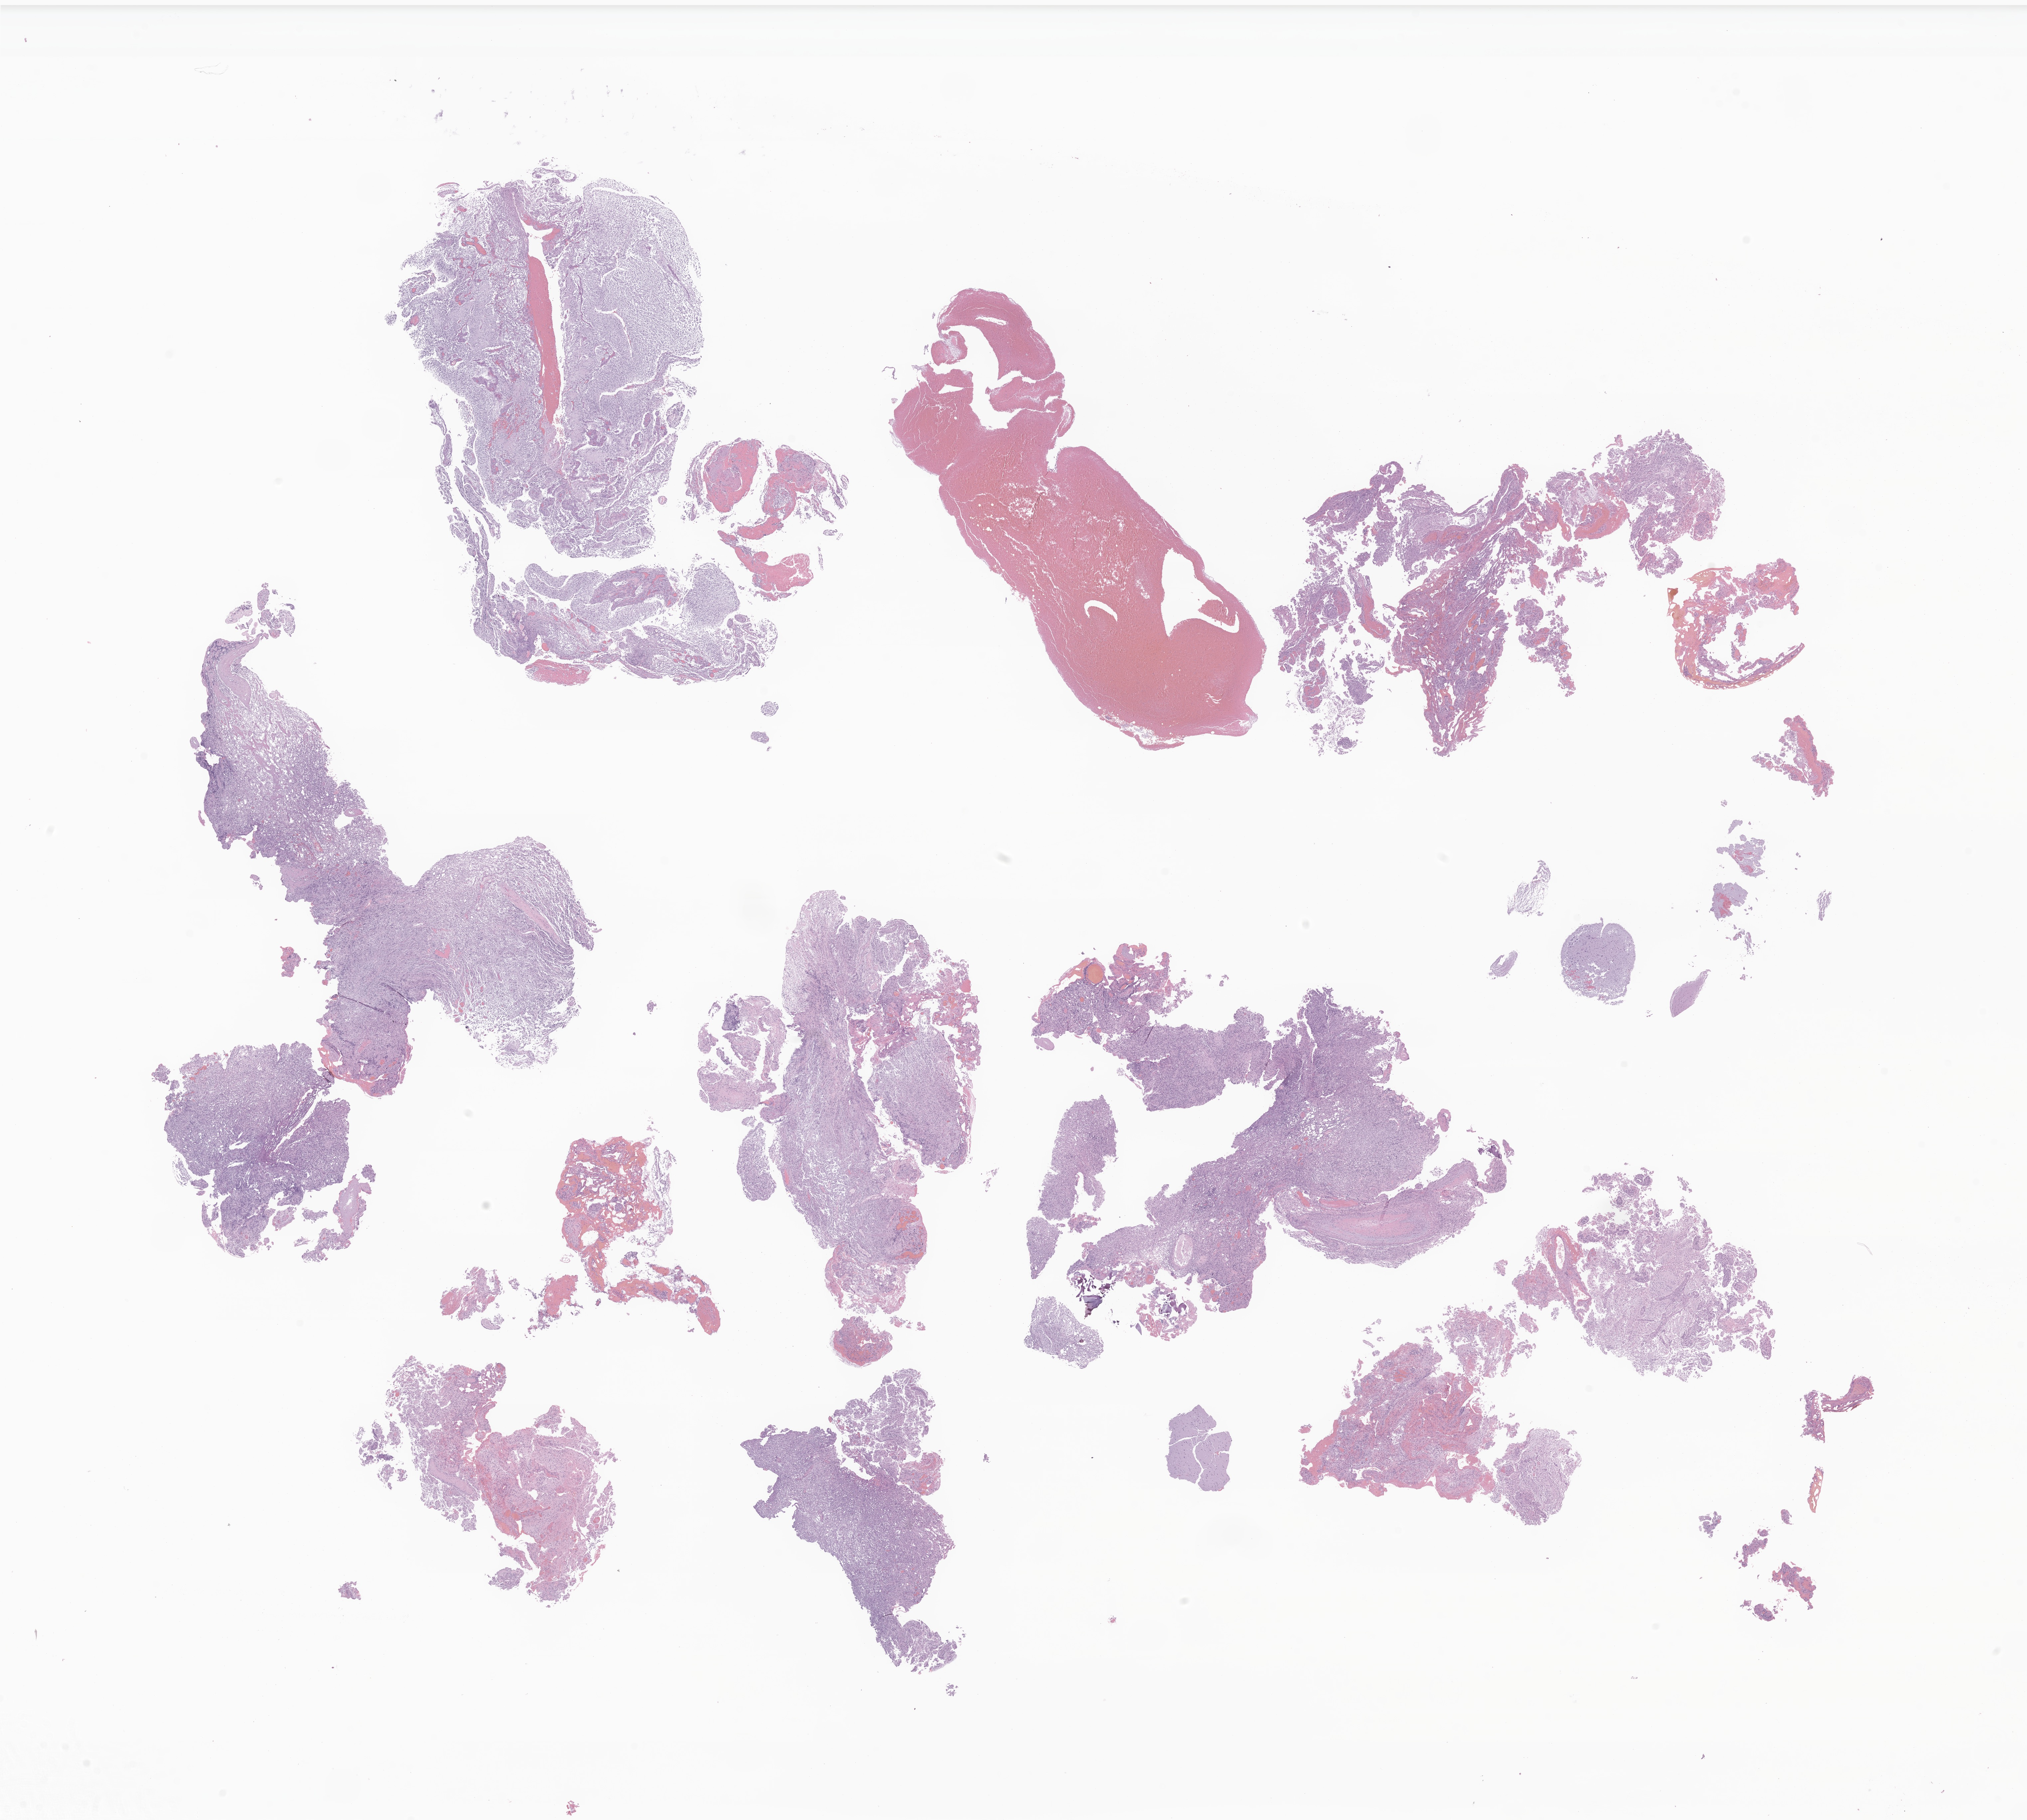
Digitized hematoxylin and eosin (H&E)-stained section of tumor tissue from the brain, a low-resolution overview of the entire scanned area, about 25.7 x 23.1 mm; formalin-fixed paraffin-embedded section. Patient female; age 161 months (13 years 5 months).
Recorded diagnosis: Ependymoma, NOS.